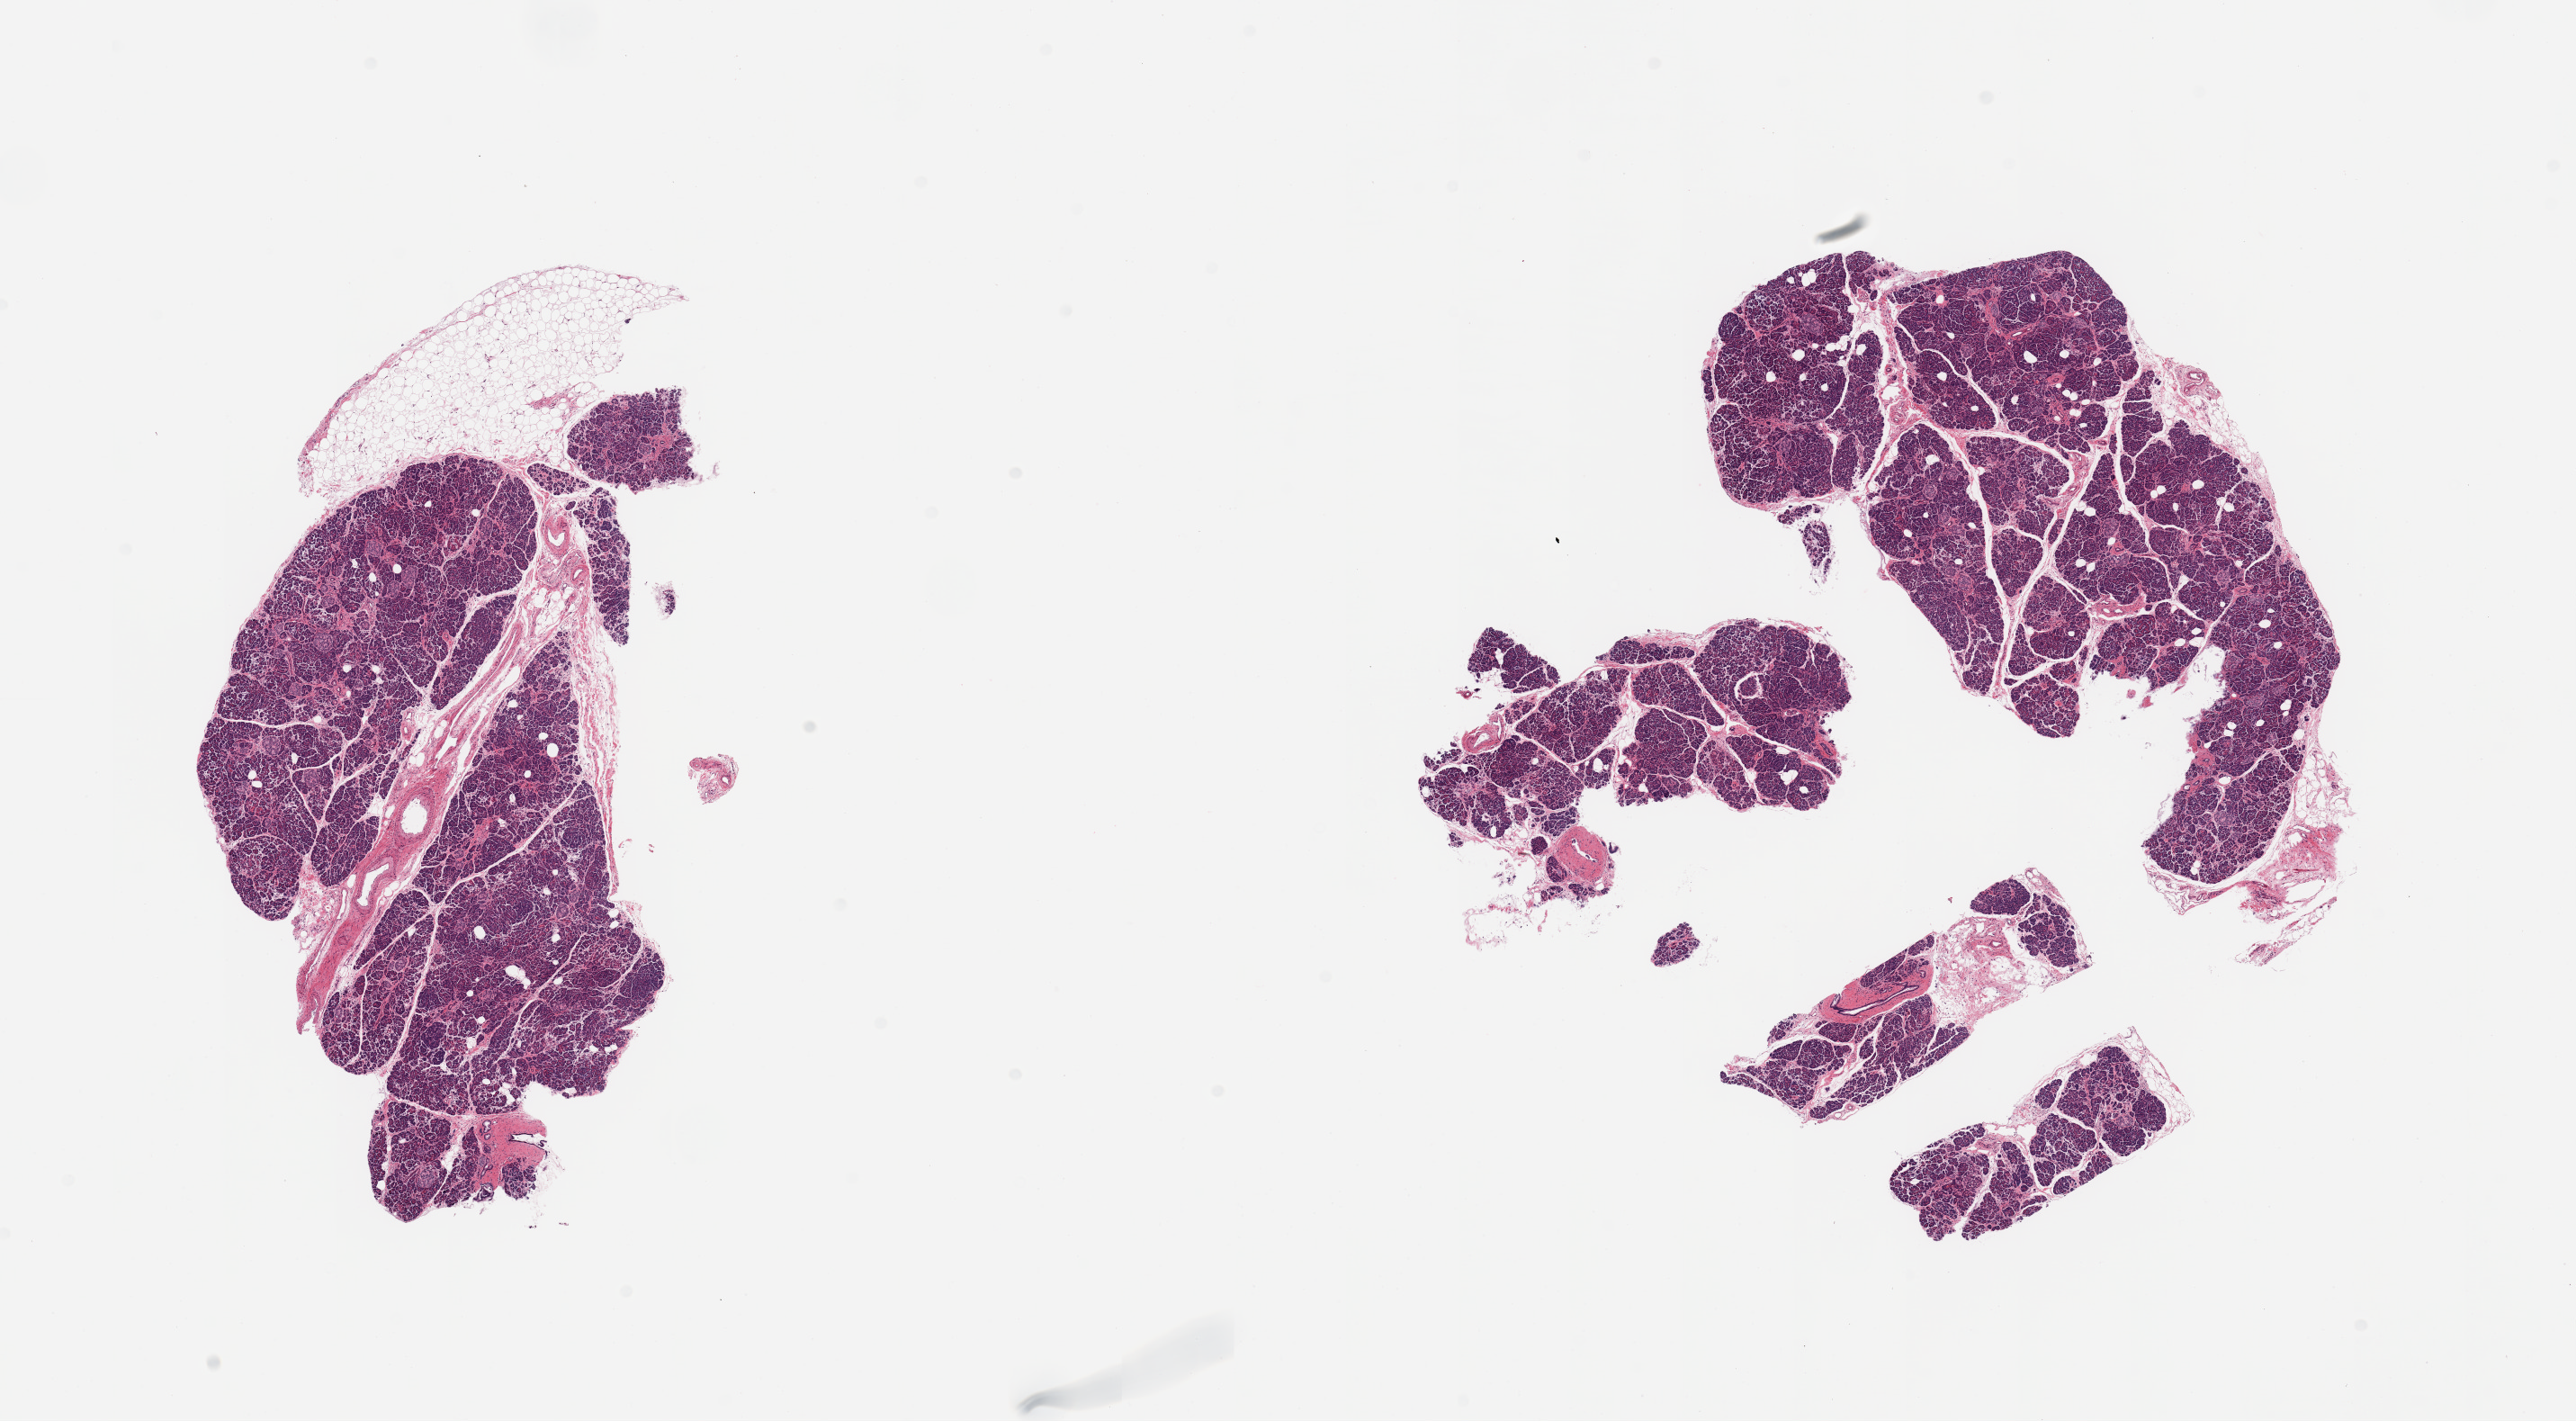
Whole-slide image, hematoxylin and eosin (H&E) stain, brightfield — shown as a low-resolution overview of the whole scanned area (about 22.6 x 12.5 mm, slide scanned at 20x), PAXgene-fixed paraffin-embedded (PFPE) section, section of pancreas (target tissue), donor tissue sample. Donor: female.
Reviewer comment on this tissue sample: 2 pieces, fragmented; 20% external fat on 1.